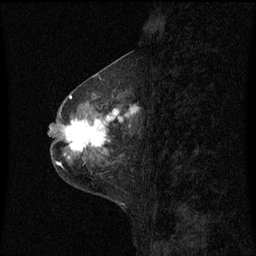
Breast MRI (dynamic contrast-enhanced), one sagittal slice. Position 25 of 60 along the scan axis. Dynamic contrast-enhanced series, image 2 of 3 at this slice position (ordered by acquisition). 1.5 T. TE 4.2 ms, TR 8.4 ms. 256 × 256 image matrix, field of view 200 × 200 mm. Patient: female, 49 years. From the clinical record (not read from this slice): setting: breast cancer imaged before/during neoadjuvant chemotherapy; receptor status: HR-positive, HER2-negative.
Structures marked on this image (semi-automatically segmented with operator editing):
- analysis volume of interest (the breast-tissue region the enhancement analysis was run in; not a lesion): bounding box (x1, y1, x2, y2) in pixels: (59, 101, 138, 158)
- tumour enhancement mask (voxels above the 70 % enhancement threshold inside the analysis volume of interest): (66, 109, 137, 152)